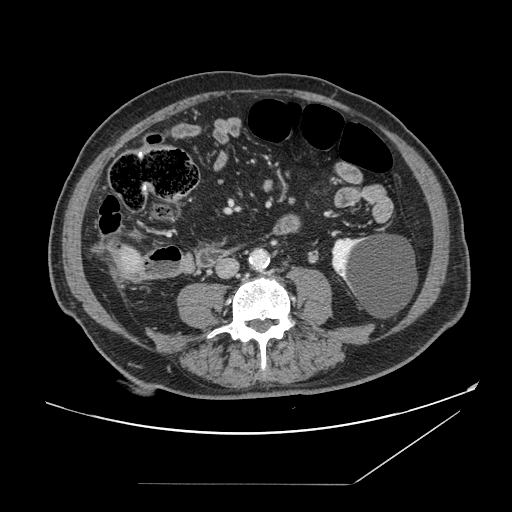
Contrast-enhanced abdominal CT, one axial slice. Slice 22 of 166 in the series (ordered by position). 120 kVp. Intravenous contrast given. Soft-tissue window (W 400 / L 40 HU). 2.5 mm slice thickness. 512 × 512 image matrix, field of view 416 × 416 mm. Male patient, age 80 years. From the clinical record (not read from this slice): diagnosis: colorectal cancer liver metastases, imaged before liver resection; multiple liver metastases: no; largest metastasis: 2.2 cm; disease in both lobes: no.
Annotated regions visible in this slice (outlined manually by an expert reader):
- liver: box from (x=111, y=245) to (x=145, y=279) px